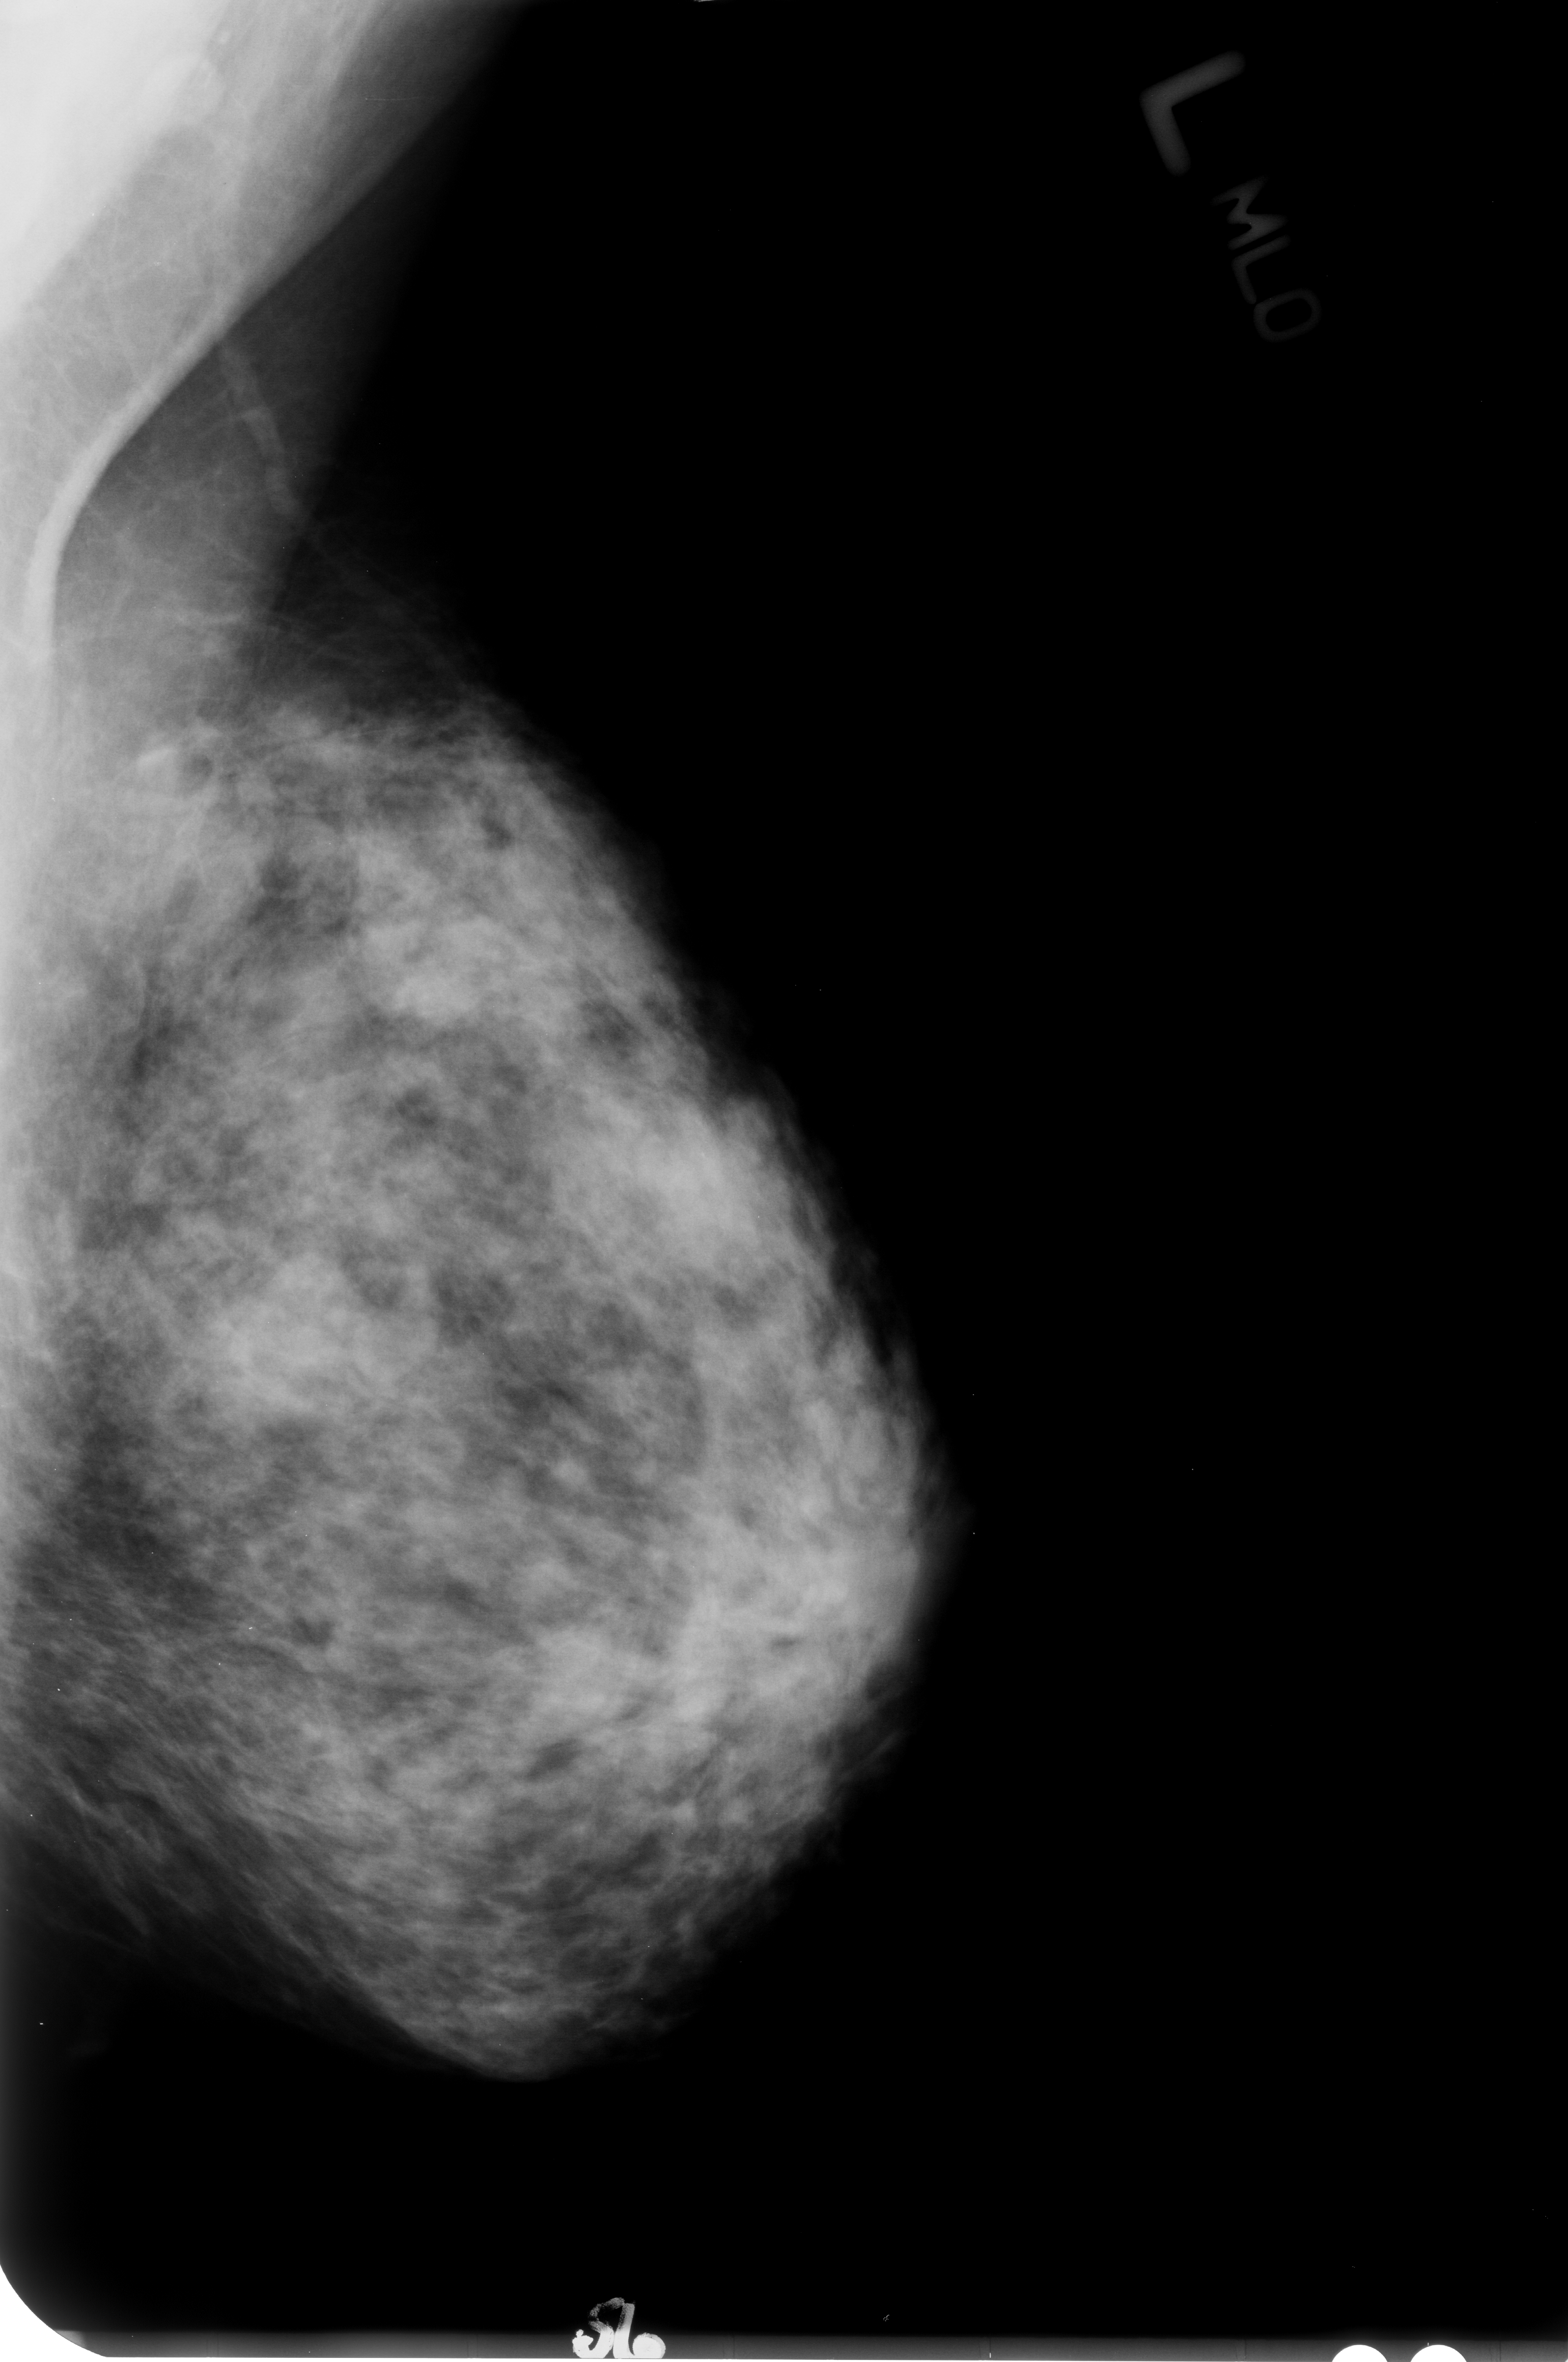
Scanned film-screen mammogram; left breast; mediolateral oblique (MLO) view.
Mass, shape oval, margins circumscribed / obscured; BI-RADS assessment category 4; subtlety rating 2 on a 1 (subtle) to 5 (obvious) scale; pathology (as recorded): benign.